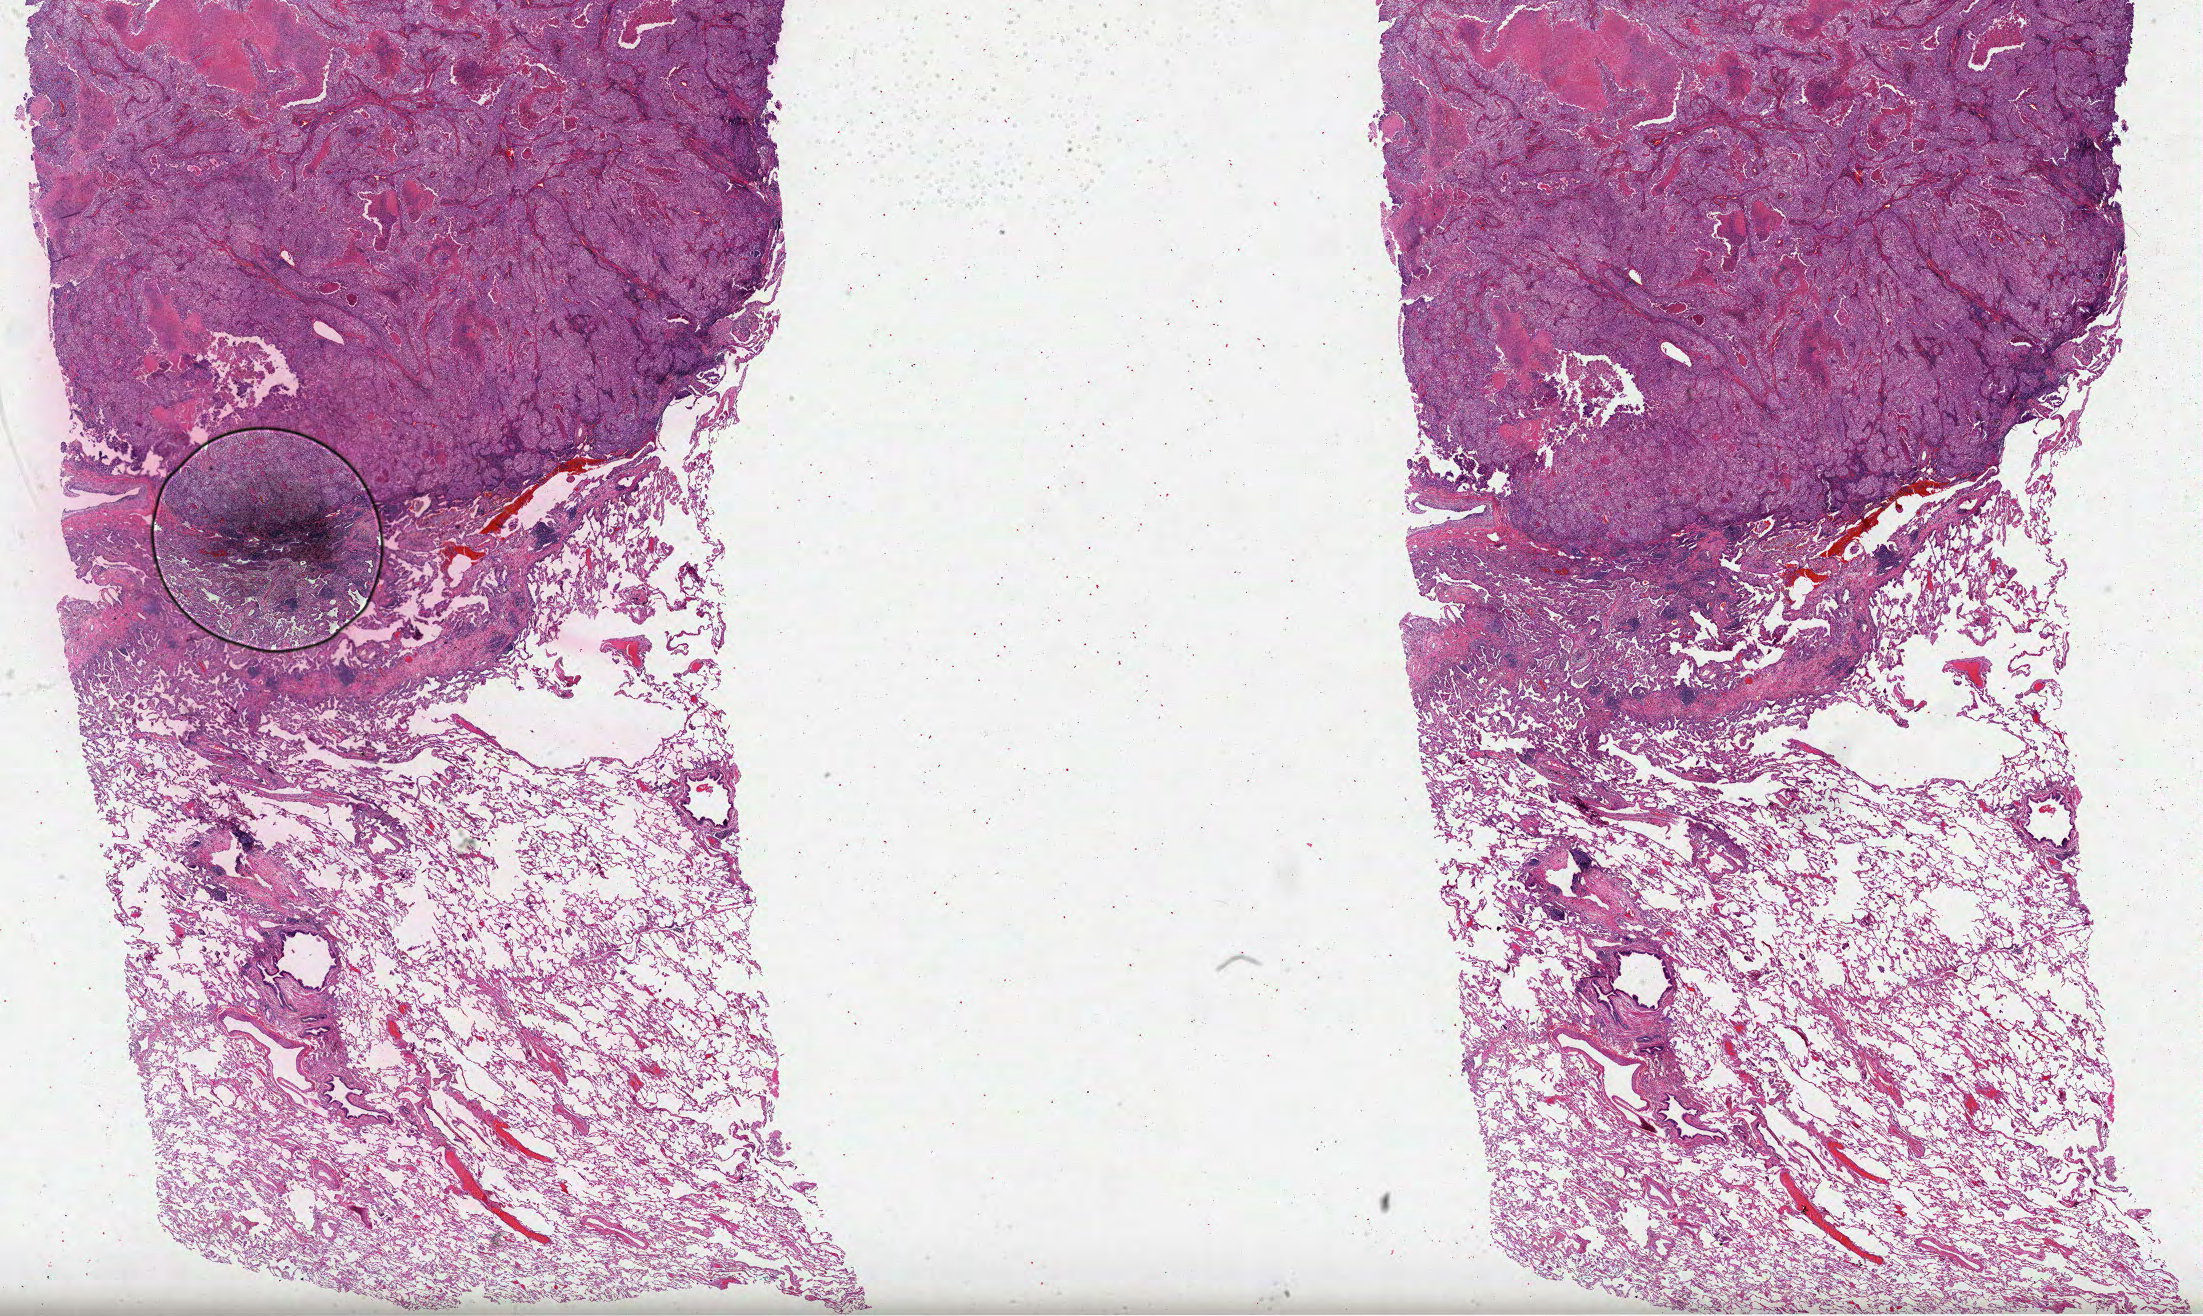
Whole-slide histology image, H&E, shown as a low-resolution overview of the whole scanned area (about 35.5 x 21.2 mm). Formalin-fixed paraffin-embedded (FFPE) diagnostic section. Lung, primary tumour sample. Female, age 81 years at initial diagnosis.
Pathologic diagnosis: Clear cell adenocarcinoma, NOS. Laterality: right. AJCC pathologic stage: IIIA (7th edition).